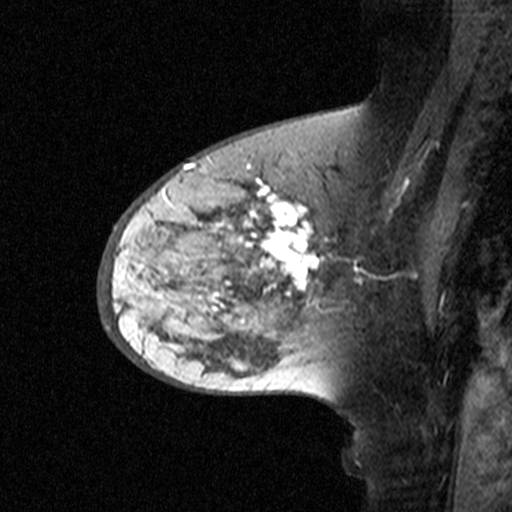
Breast MRI (dynamic contrast-enhanced), one sagittal slice. Slice 26 of 44 in the series (ordered by position). Dynamic contrast-enhanced study with each time point stored as its own series, time point 2 of 3 at this slice position (early post-contrast, ordered by acquisition time). 1.5 T. TE 4.5 ms, TR 11 ms. 512 × 512 image matrix, field of view 200 × 200 mm. Patient: female, 65 years. Case-level facts recorded for this patient, not image findings: setting: breast cancer imaged before/during neoadjuvant chemotherapy; receptor status: HER2-positive.
Structures marked on this image (semi-automatically segmented with operator editing):
- analysis volume of interest (the breast-tissue region the enhancement analysis was run in; not a lesion): bounding box <160,172,329,345> (left, top, right, bottom; pixels)
- tumour enhancement mask (voxels above the 90 % enhancement threshold inside the analysis volume of interest): <195,177,320,310>